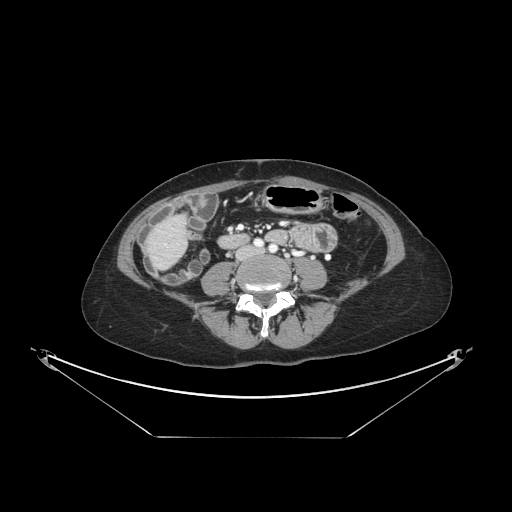
Contrast-enhanced abdominal CT, one axial slice; slice 24 of 148 in the series (ordered by position); 120 kVp; intravenous contrast given; soft-tissue window (W 400 / L 40 HU); 512 × 512 image matrix, field of view 500 × 500 mm. Female patient, age 73 years. From the clinical record (not read from this slice): diagnosis: colorectal cancer liver metastases, imaged before liver resection; multiple liver metastases: no; largest metastasis: 1 cm.
Annotated regions visible in this slice (expert manual segmentation):
- liver: box from (x=151, y=217) to (x=186, y=266) px
- planned liver remnant (the part of the liver to remain after resection): (x=169, y=217)–(x=184, y=232)